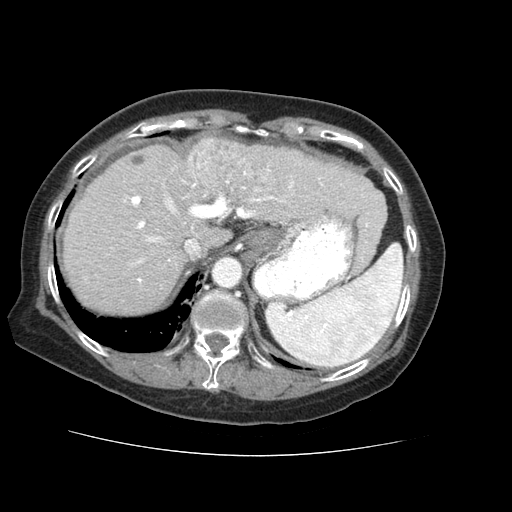
Contrast-enhanced abdominal CT (liver protocol), one axial slice. Position 48 of 73 along the scan axis. Reconstruction kernel STANDARD. Soft-tissue window (W 400 / L 40 HU). 512 × 512 image matrix. Case-level facts recorded for this patient, not image findings: diagnosis: hepatocellular carcinoma (patient treated with transarterial chemoembolisation; whether this scan precedes or follows treatment is not stated here); TNM stage (as recorded): Stage-IVB; Child-Pugh class: A; tumour differentiation: well differentiated; tumour nodularity: uninodular.
Annotated regions visible in this slice (semi-automatically segmented with operator editing):
- liver parenchyma outside the tumour (the mass and vessels are separate outlines, so this box may not span the whole liver): bounding box [x1, y1, x2, y2] px = [64, 136, 384, 314]
- mass: [185, 138, 252, 187]
- liver vessels: [124, 169, 368, 282]